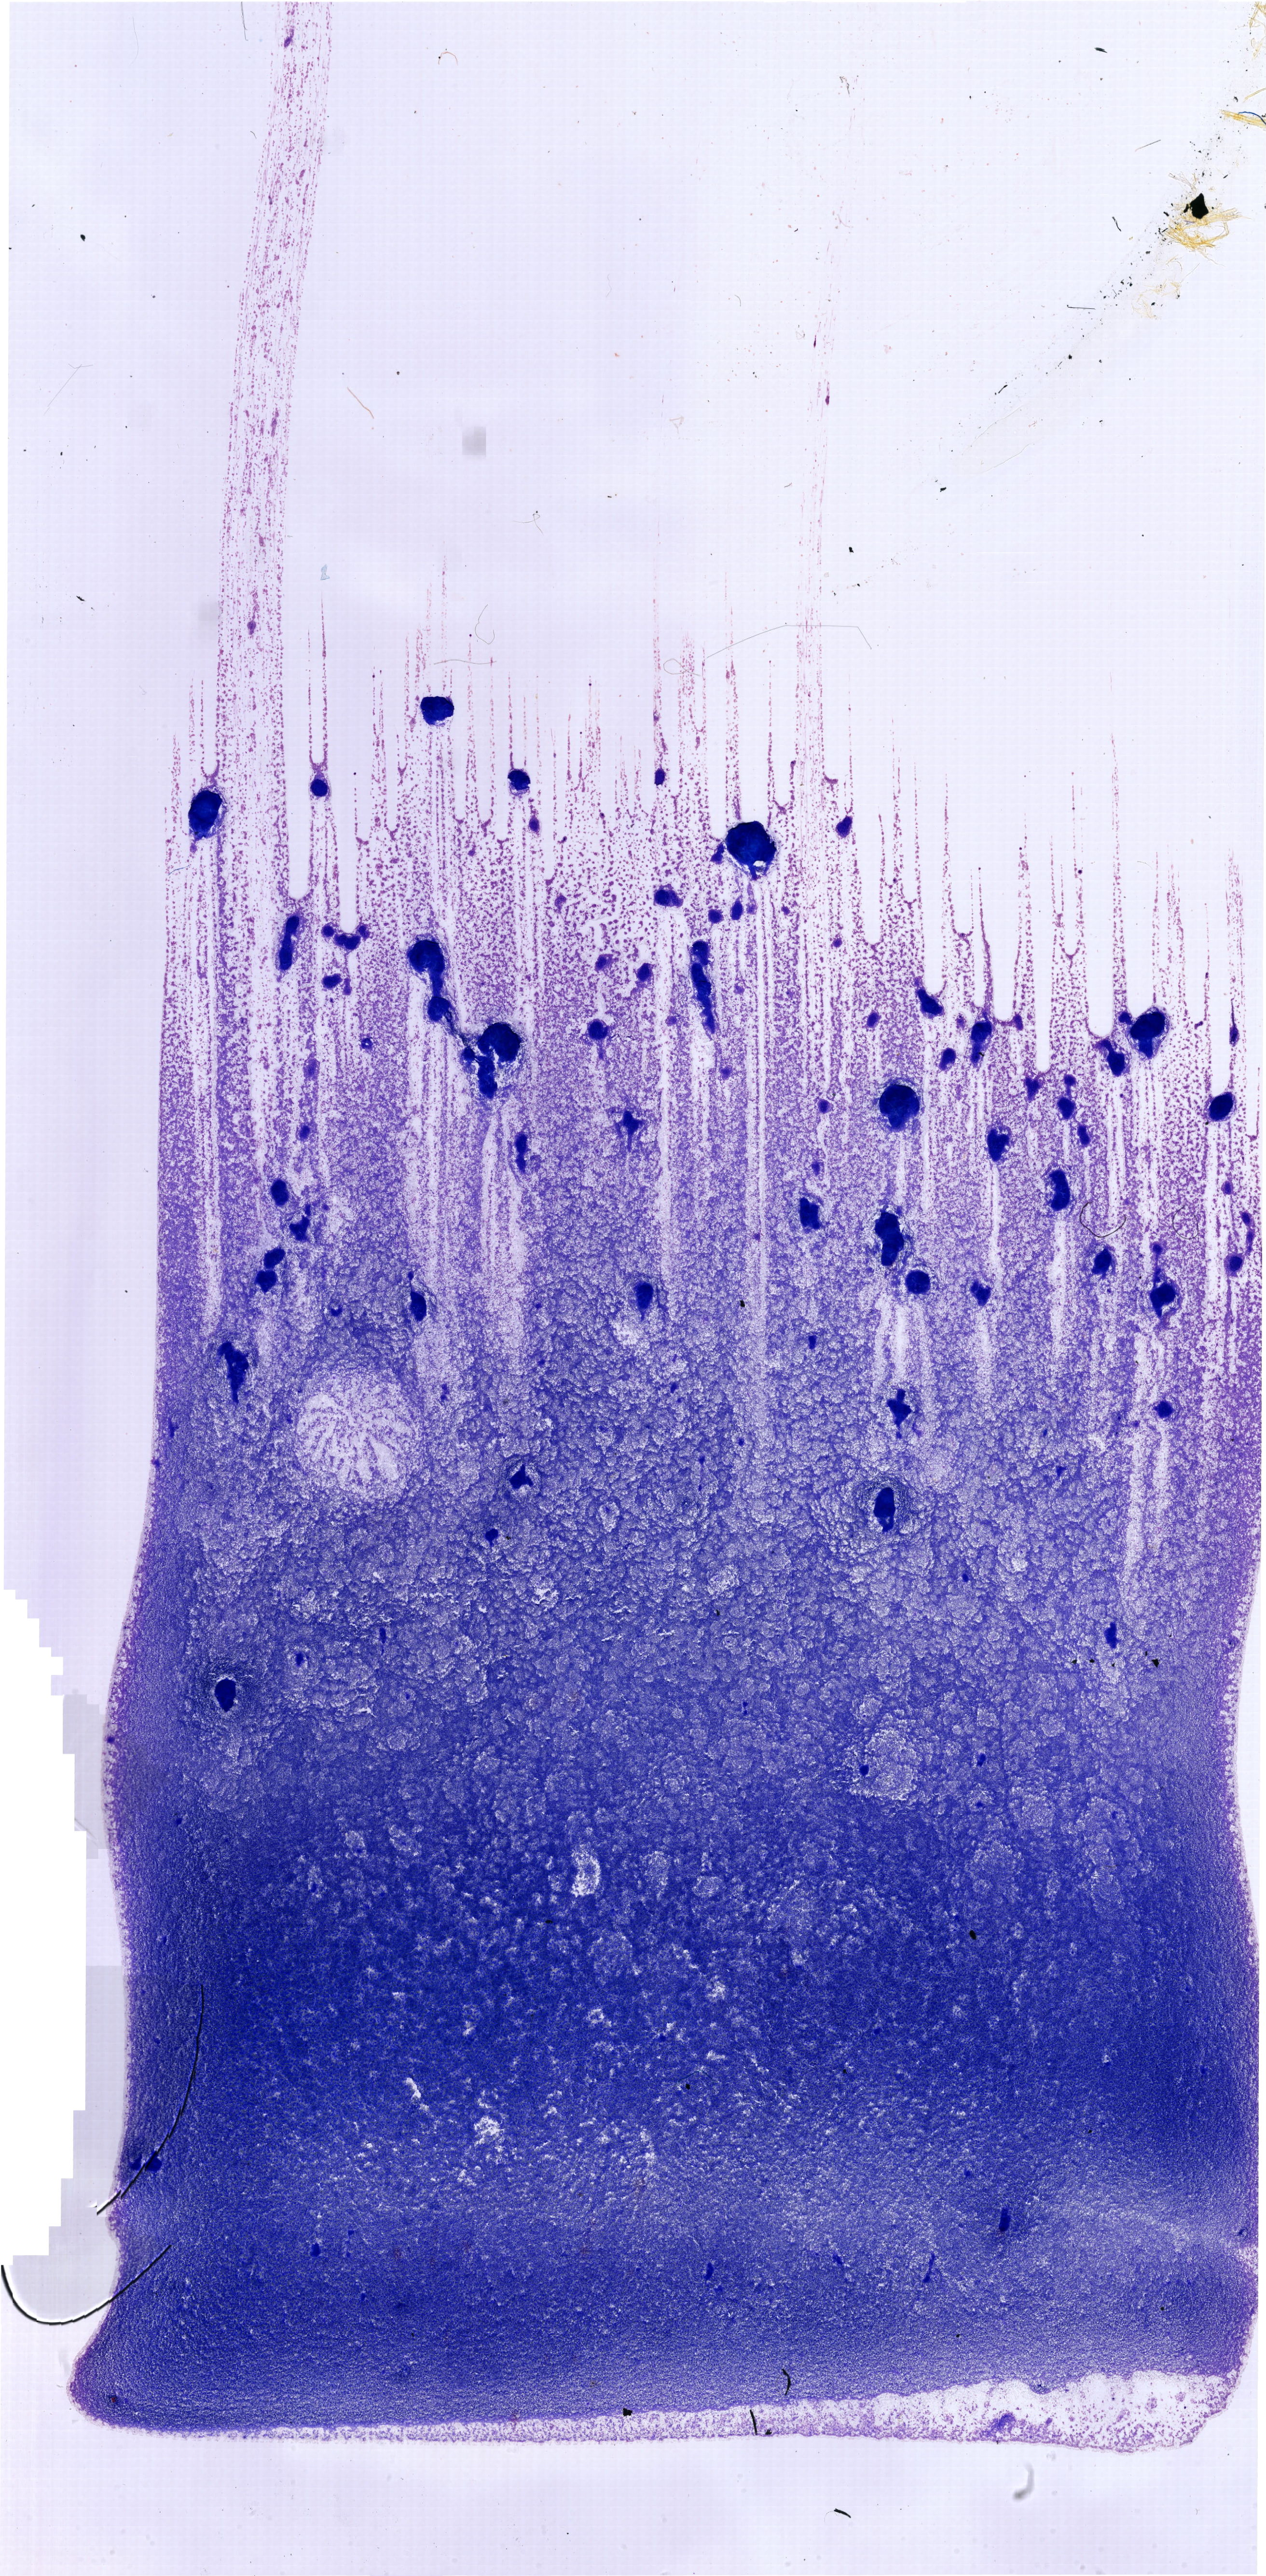
Whole-slide image of a May-Grünwald-Giemsa (MGG)-stained bone marrow aspirate smear — a low-resolution overview of the entire scanned area, about 20.5 x 41.7 mm. Patient sex: male.
Diagnosis: Mixed Phenotype Acute Leukemia, B/Myeloid.